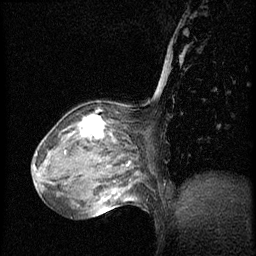
Breast MRI (dynamic contrast-enhanced), one sagittal slice. Position 21 of 56 along the scan axis. Dynamic contrast-enhanced series, image 2 of 3 at this slice position (ordered by acquisition). 1.5 T. TE 4.2 ms, TR 20.4 ms. 2 mm slice thickness. 256 × 256 image matrix, field of view 200 × 200 mm. Patient: female, 64 years. From the clinical record (not read from this slice): setting: breast cancer imaged before/during neoadjuvant chemotherapy; receptor status: HR-positive, HER2-negative.
Structures marked on this image (semi-automatic segmentation, software-assisted and operator-edited):
- analysis volume of interest (the breast-tissue region the enhancement analysis was run in; not a lesion): bounding box [x1, y1, x2, y2] px = [48, 101, 142, 186]
- tumour enhancement mask (voxels above the 70 % enhancement threshold inside the analysis volume of interest): [80, 114, 106, 139]